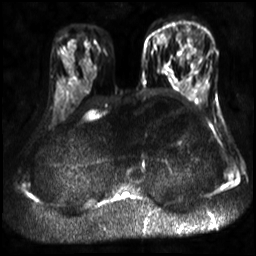
Breast MRI, one axial slice. Position 16 of 30 along the scan axis. Diffusion-weighted series; image 2 of 4 stored at this slice position (different b-values; order by instance number). 3 T. 256 × 256 image matrix, field of view 320 × 320 mm. Female patient.
Structures marked on this image (expert manual segmentation):
- tumour on diffusion-weighted imaging: bounding box <182,30,202,58> (left, top, right, bottom; pixels)